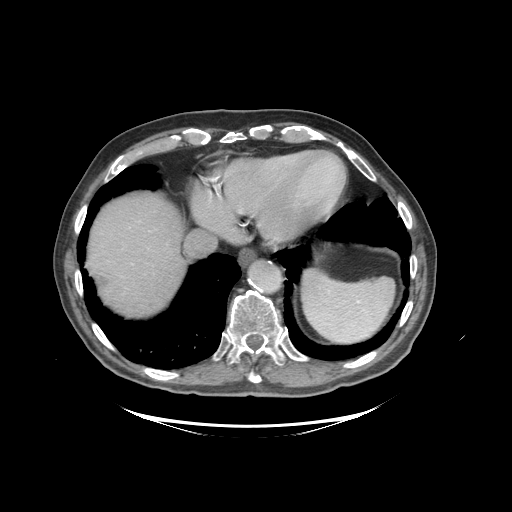
Contrast-enhanced abdominal CT (liver protocol), one axial slice. Slice 85 of 99 in the series (ordered by position). Soft-tissue window (W 400 / L 40 HU). 2.5 mm slice thickness. 512 × 512 image matrix, field of view 460 × 460 mm. From the clinical record (not read from this slice): diagnosis: hepatocellular carcinoma (patient treated with transarterial chemoembolisation; whether this scan precedes or follows treatment is not stated here); TNM stage (as recorded): Stage-I; Child-Pugh class: A; tumour nodularity: uninodular.
Structures marked on this image (semi-automatically segmented with operator editing):
- abdominal aorta: box from (x=251, y=263) to (x=281, y=292) px
- liver parenchyma outside the tumour (the mass and vessels are separate outlines, so this box may not span the whole liver): (x=88, y=194)–(x=186, y=316)